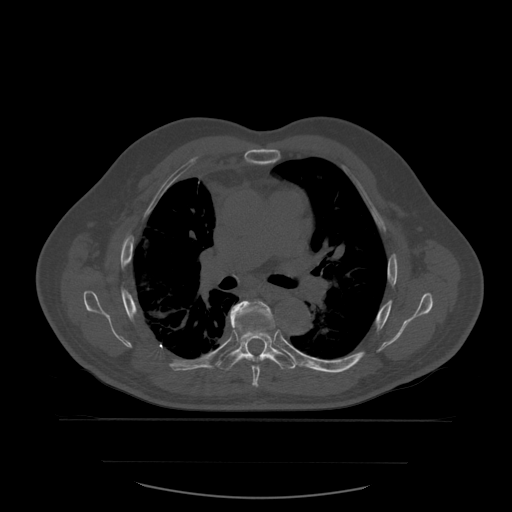
CT including the spine, one axial slice; slice 393 of 590 in the series (ordered by position); bone window (W 1800 / L 400 HU); 1.25 mm slice thickness; 512 × 512 image matrix, field of view 479 × 479 mm. Patient age 71 years. Case-level facts recorded for this patient, not image findings: primary cancer: lung; vertebrae with lytic lesions (as recorded): T1, T2, L5, S1.
Annotated regions visible in this slice (semi-automatic segmentation, software-assisted and operator-edited):
- T6 vertebra: bounding box <231,300,273,388> (left, top, right, bottom; pixels)
- T7 vertebra: <218,303,297,371>